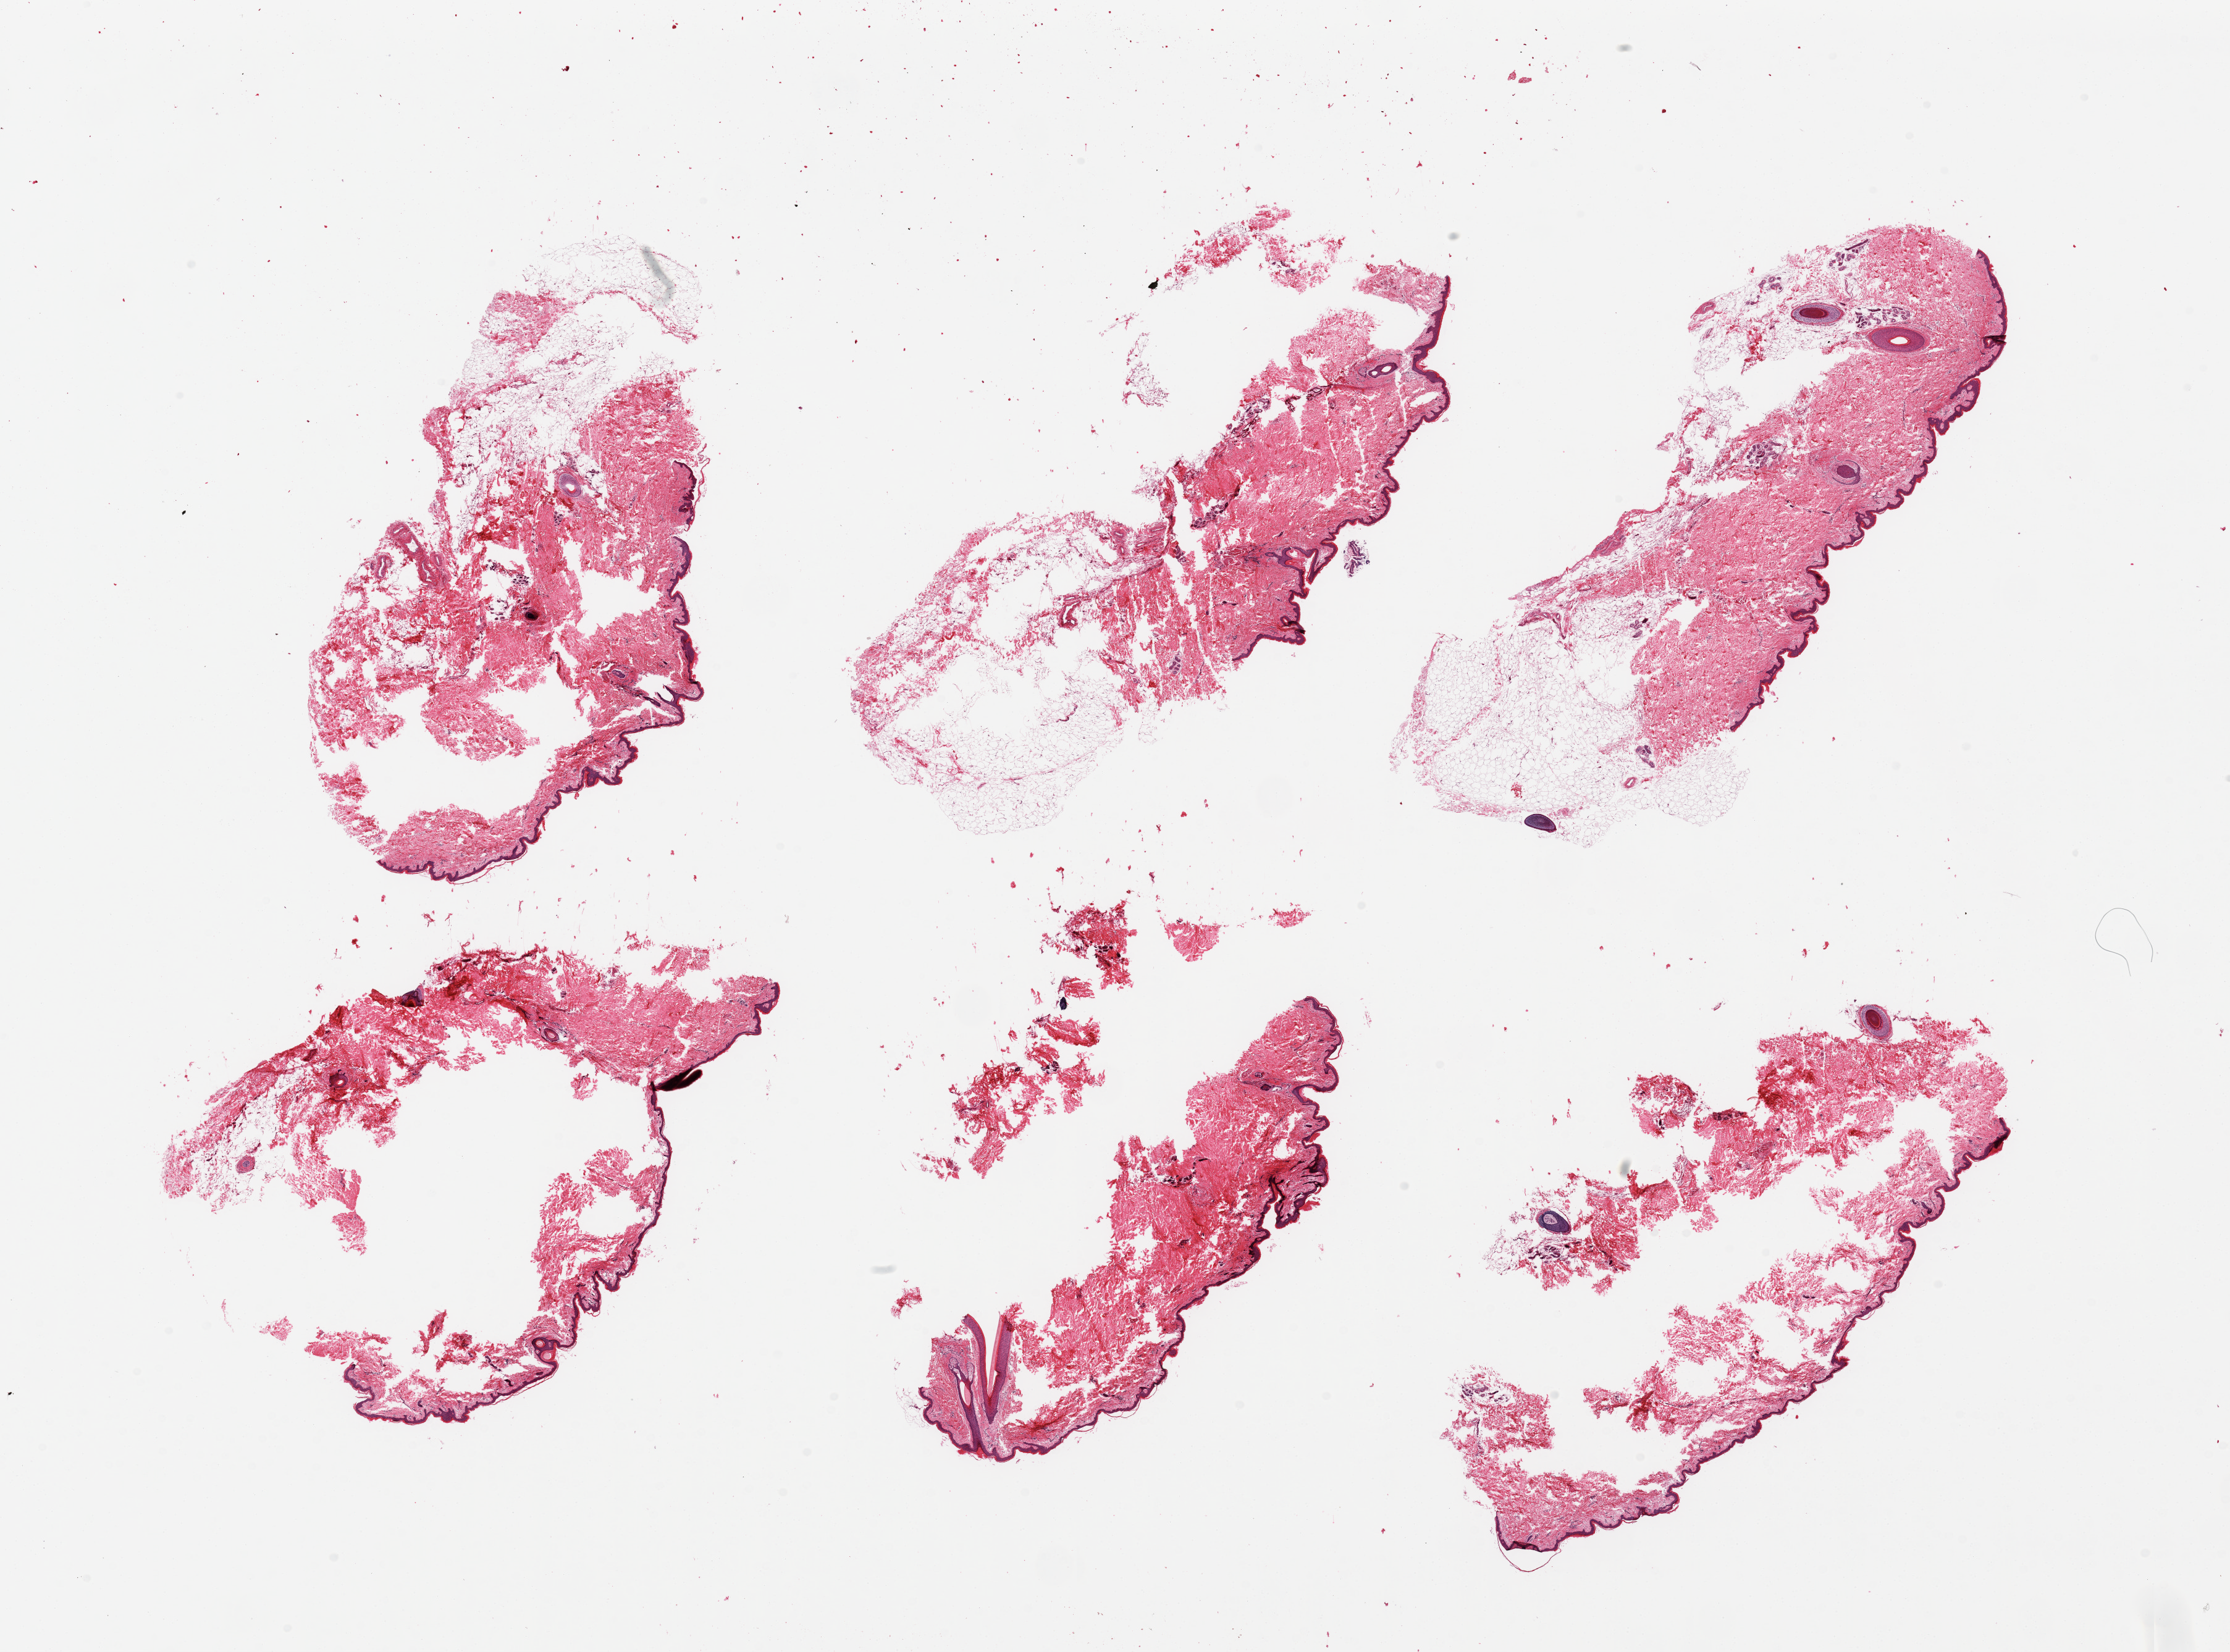
Digitized hematoxylin and eosin (H&E)-stained section, shown as a low-resolution overview of the whole scanned area (about 28.5 x 21.2 mm); PAXgene-fixed, paraffin-embedded tissue; section of skin of suprapubic region (target tissue); tissue donor sample. Donor sex: female.
• reviewer comment on this tissue sample: 6 severely fragmented pieces; 25% subcutaneous fat in 3 pieces